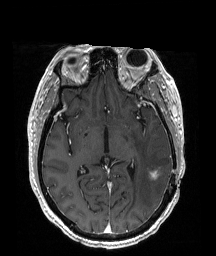
Brain MRI from a brain-tumour surgery series, one axial slice; position 101 of 192 along the scan axis; T1-weighted post-contrast; 1 mm slice thickness; 216 × 256 image matrix. From the clinical record (not read from this slice): histopathology: Glioblastoma; WHO grade: 4; IDH mutation: no; tumour location: Left Temporoparietal.
Outlined on this slice (outlined manually by an expert reader):
- tumour: box from (x=161, y=168) to (x=170, y=177) px